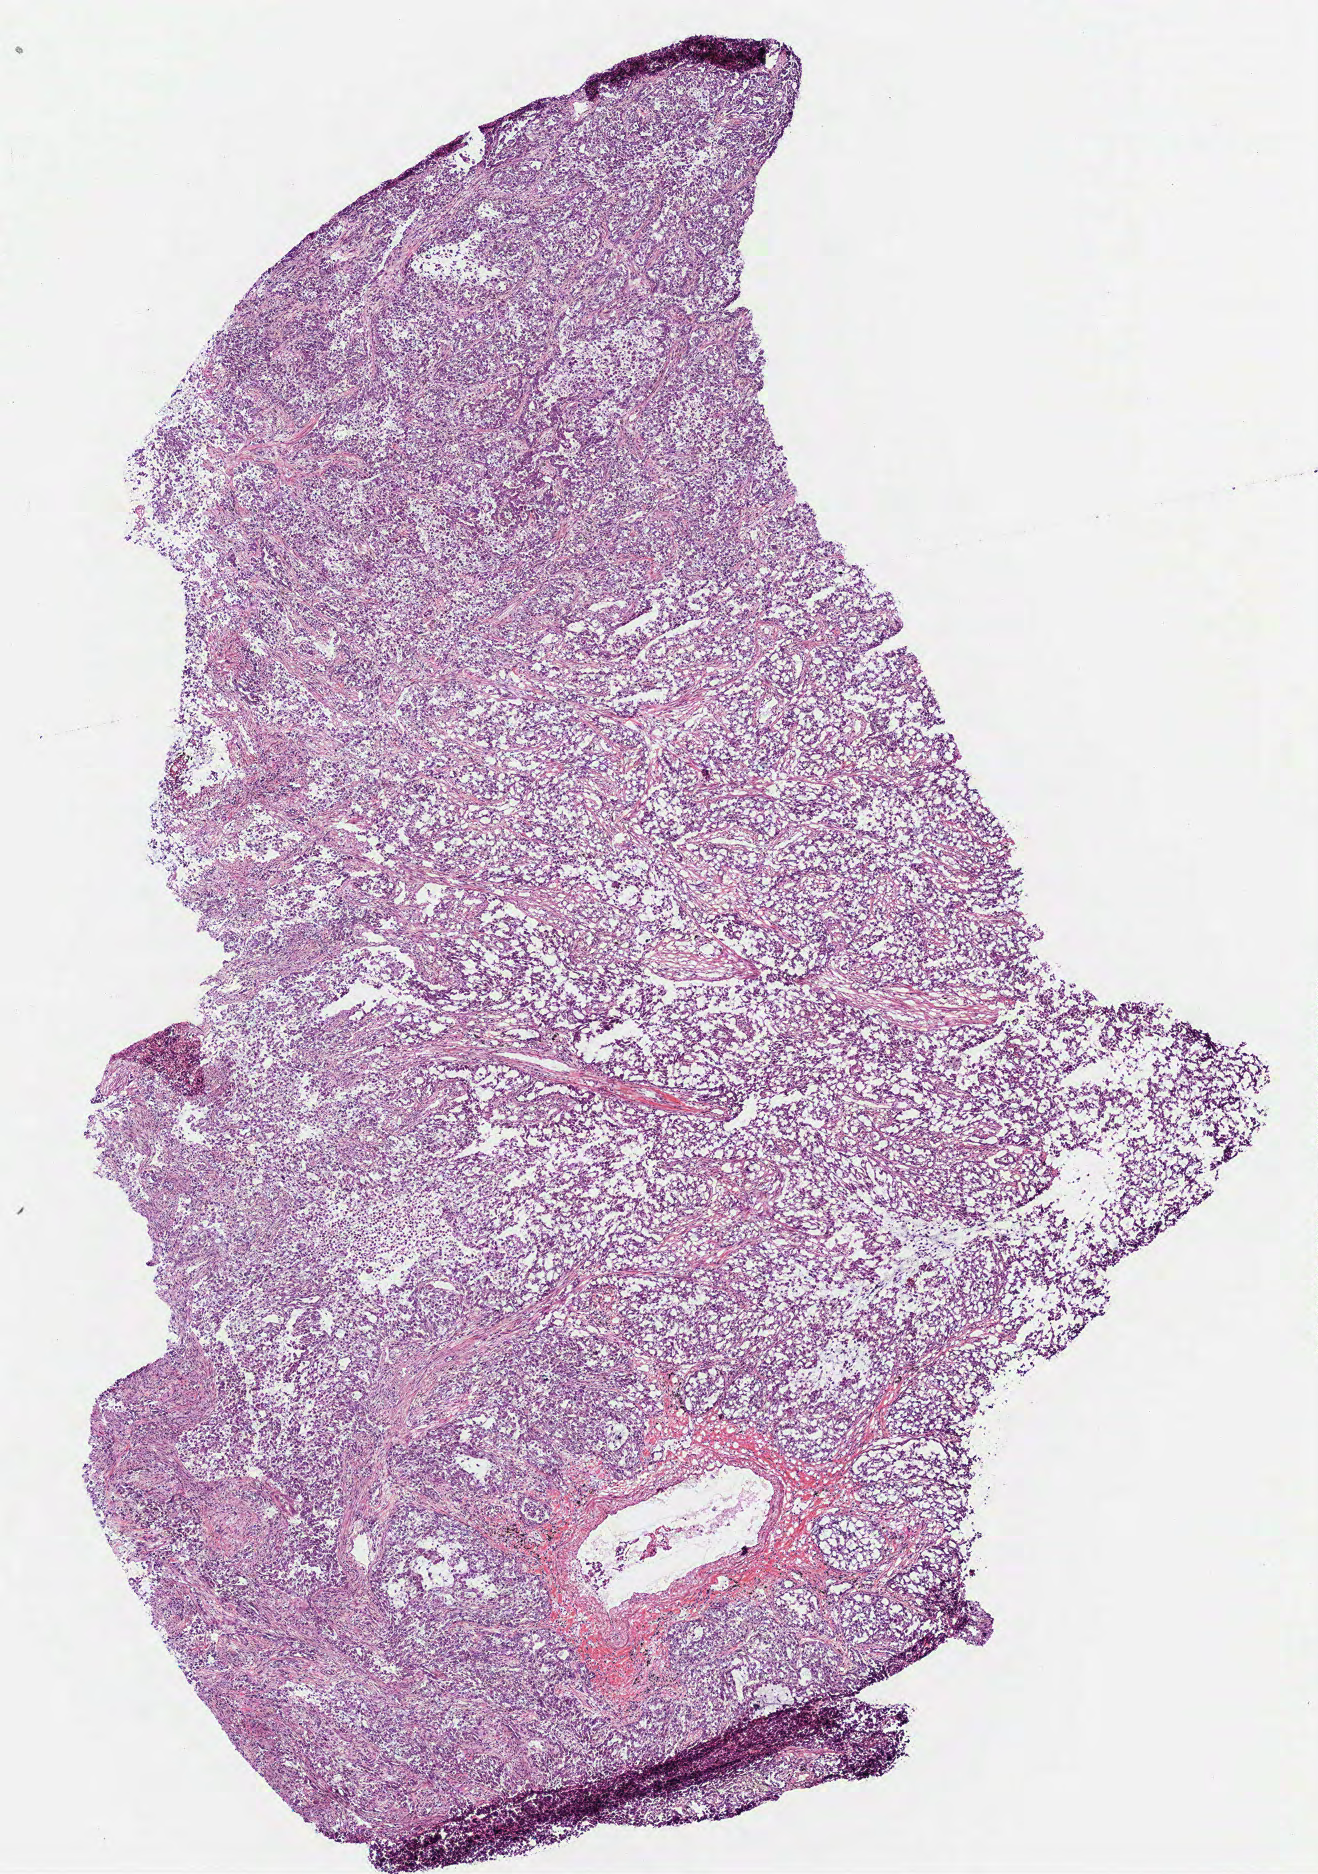
H&E-stained whole-slide image, low-resolution overview of the scanned area, about 5.3 x 7.6 mm (slide scanned at 40x), frozen section from the bottom of the tissue portion, lung, primary tumour sample. Male patient; age at initial diagnosis 45 years. Composition of this section per pathologist review: tumour cells 100%, tumour nuclei 80%, normal cells 0%, stromal cells 0%, necrosis 0%. Inflammatory infiltration, as recorded: lymphocyte infiltration 5%, monocyte infiltration 5%, neutrophil infiltration 0%.
Pathologic diagnosis: Adenocarcinoma, NOS (upper lobe, lung). AJCC pathologic stage: IB (6th edition).